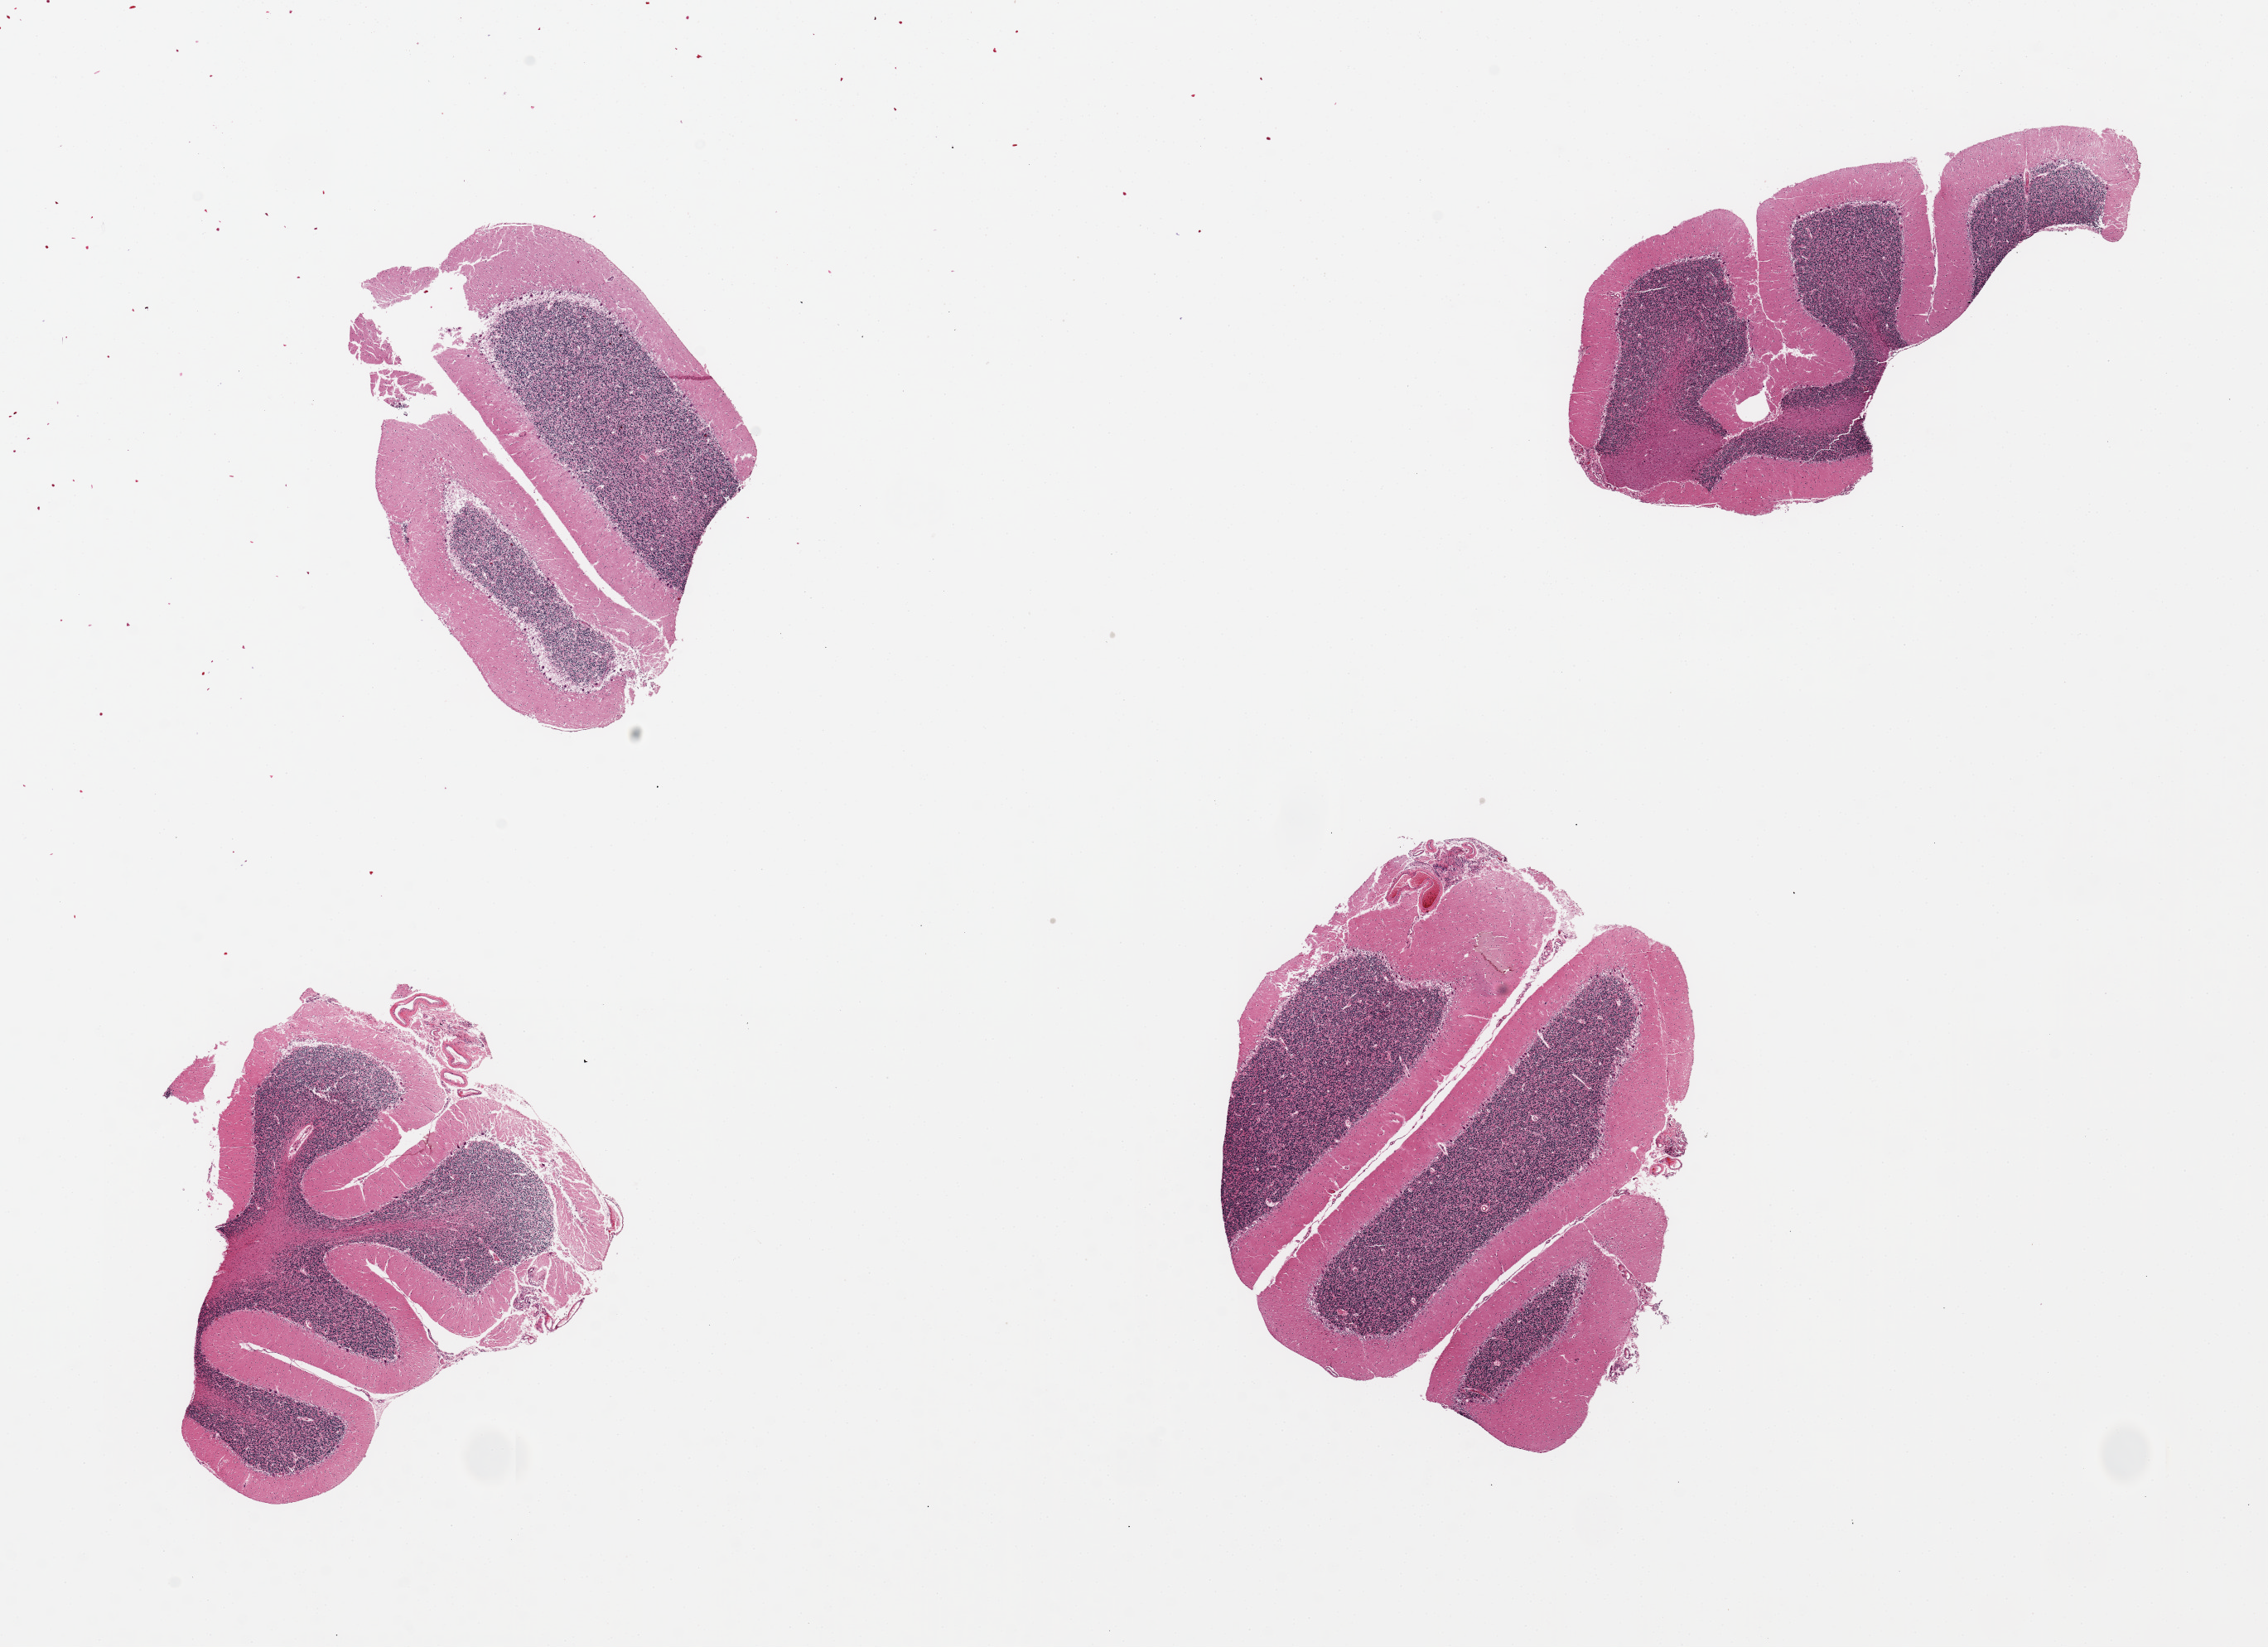
Digitized haematoxylin and eosin-stained section, whole scanned area (about 21.7 x 15.7 mm) shown as a low-resolution overview, PAXgene-fixed, paraffin-embedded tissue, sampled site (target tissue): cerebellum, donor tissue sample.
• pathologist's review note for this sample: 4 pieces up to 6x3mm; anoxic changes